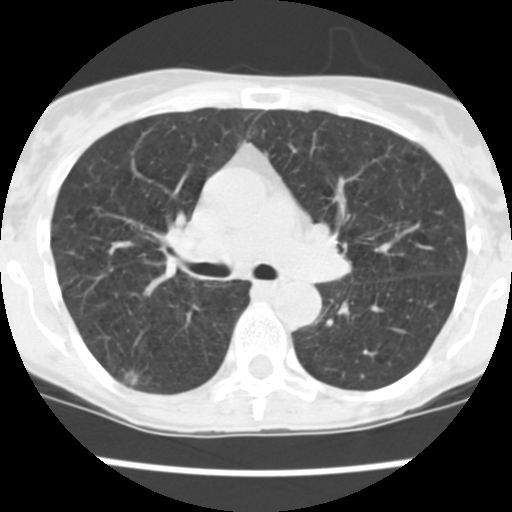
Low-dose screening chest CT, one axial slice. Position 151 of 252 along the scan axis. Reconstruction kernel STANDARD. Lung window (W 1500 / L -600 HU). 512 × 512 image matrix.
Annotated regions visible in this slice (manually delineated by an expert):
- lesion 1 (tumor, upper lobe of right lung): box from (x=126, y=372) to (x=137, y=385) px